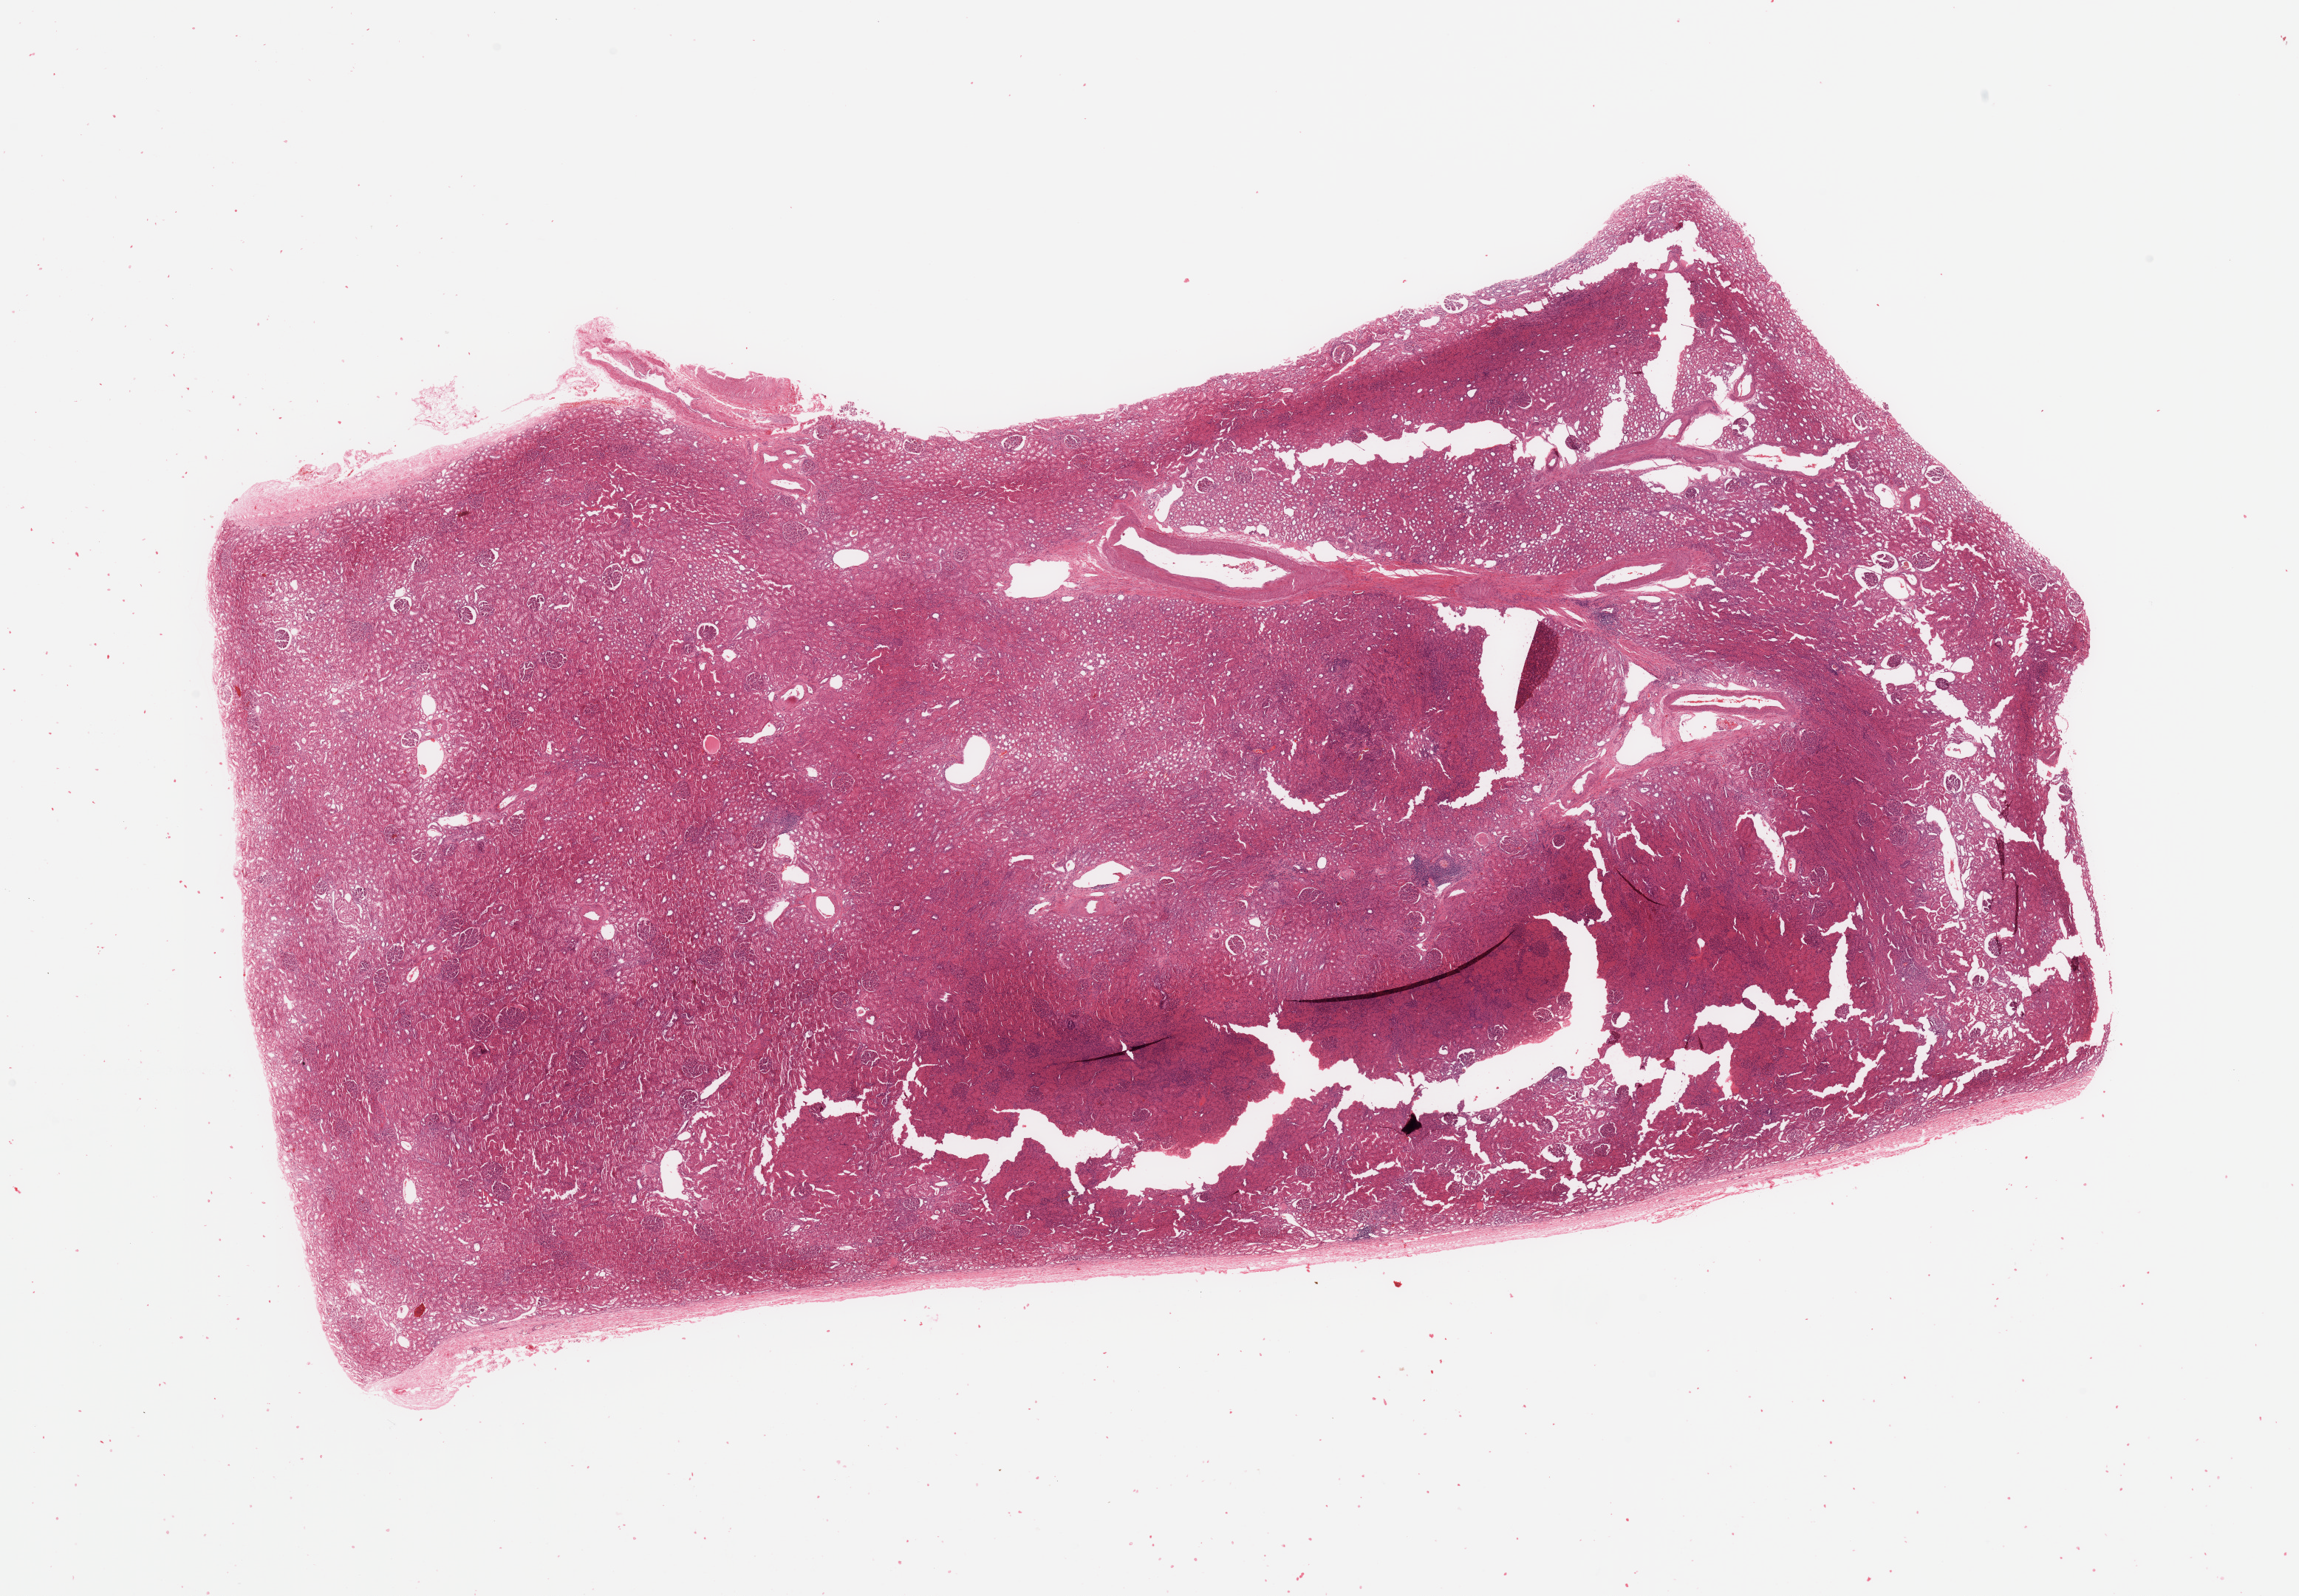
Whole-slide histology image, H&E, shown as a low-resolution overview of the whole scanned area (about 24.6 x 17.1 mm). Normal (non-tumour) tissue sample, kidney. 57-year-old female patient.
• this section: normal (non-tumour) tissue from the same patient
• patient diagnosis: Renal cell carcinoma, NOS